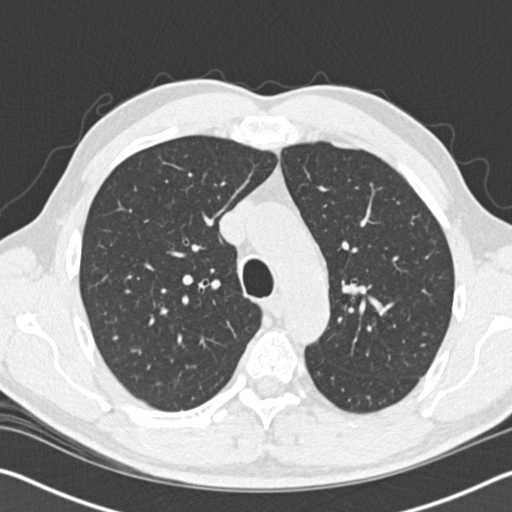
Axial slice from a low-dose chest CT screening exam; baseline screening round; lung window (W 1500 / L -600 HU); 2 mm slice thickness; 120 kVp. Male, age 61 years at enrolment.
Expert-annotated lung lesion, bounding box [x1, y1, x2, y2] px = [340, 271, 375, 318]. The screening reader recorded 2 non-calcified nodules or masses ≥4 mm on this exam (right middle lobe, left upper lobe); which of them this box marks is not recorded. Official screen result: positive, change unspecified: nodule(s) >= 4 mm or enlarging nodule(s), mass(es), or other non-specific abnormalities suspicious for lung cancer. Lung cancer was diagnosed 183 days after this screen: small cell carcinoma, NOS, left upper lobe, stage IIIB (AJCC 6th edition), 100 mm at pathology.